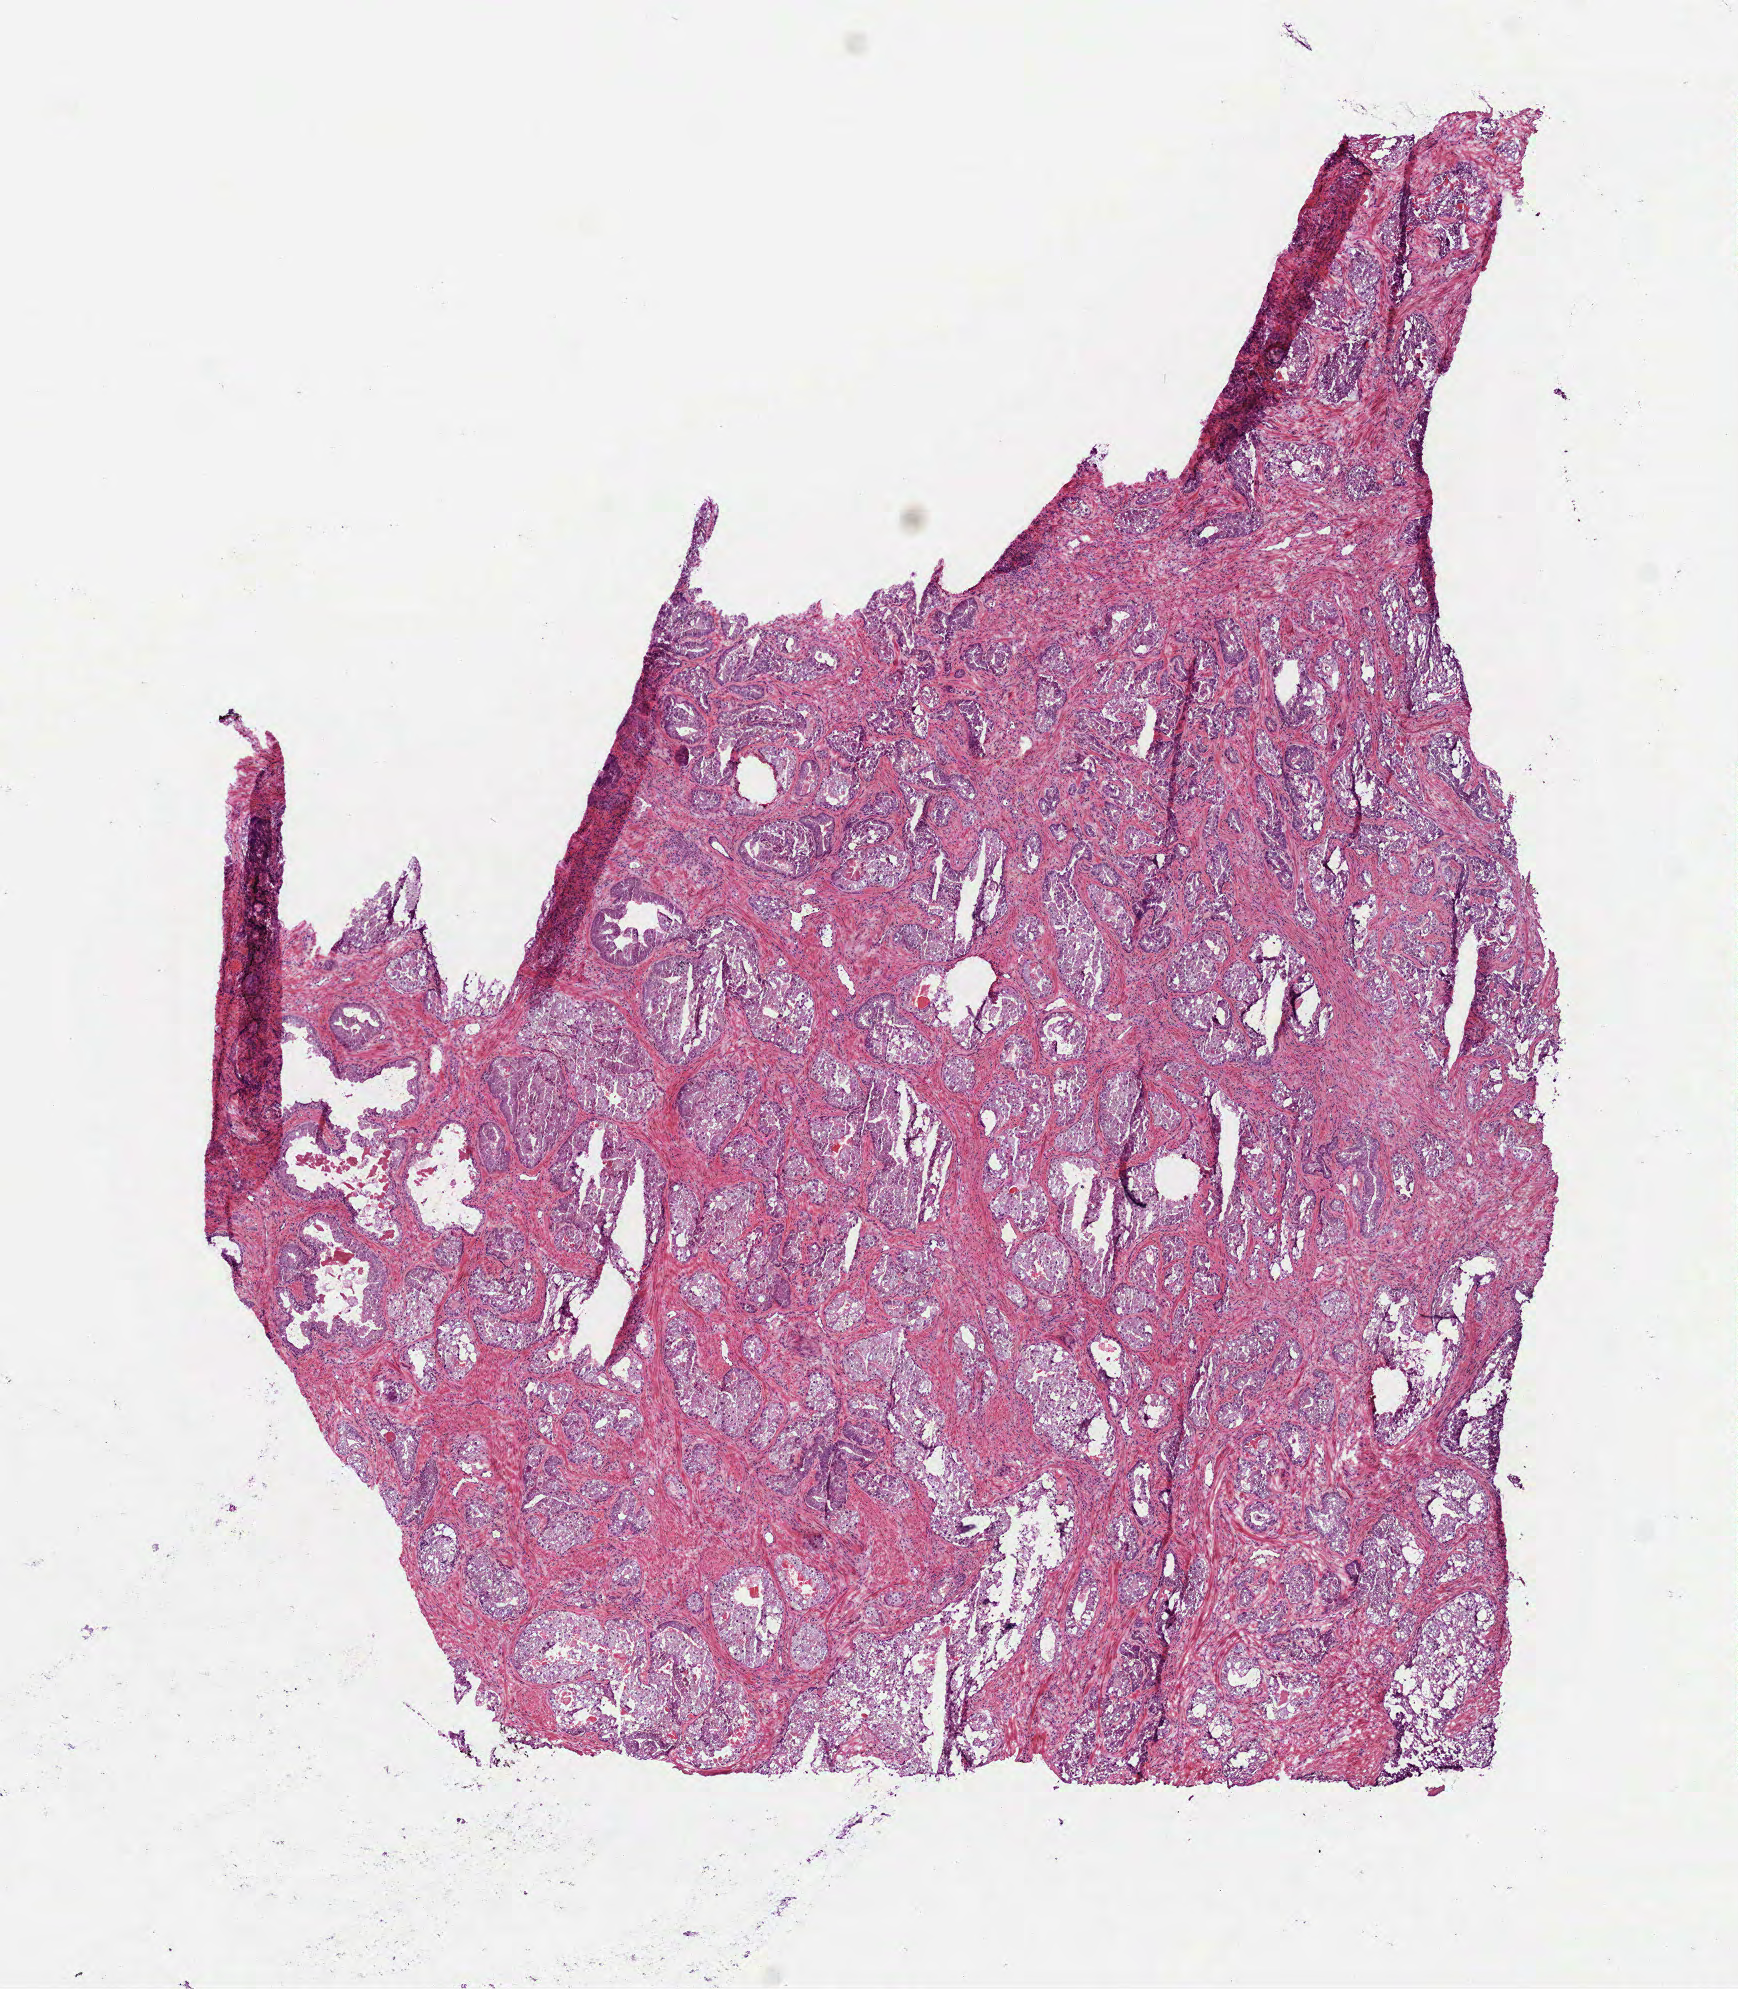
Whole-slide histology image, H&E-stained — shown as a low-resolution overview of the whole scanned area (about 7.0 x 8.0 mm). Frozen section from the bottom of the tissue portion. Primary tumour sample from the prostate. Male, age 62 years at initial diagnosis. Gleason score: 9 (4+5). Composition of this section per pathologist review: tumour cells 50%, tumour nuclei 50%, normal cells 5%, stromal cells 45%, necrosis 0%.
Diagnosis: Acinar cell carcinoma (prostate gland).